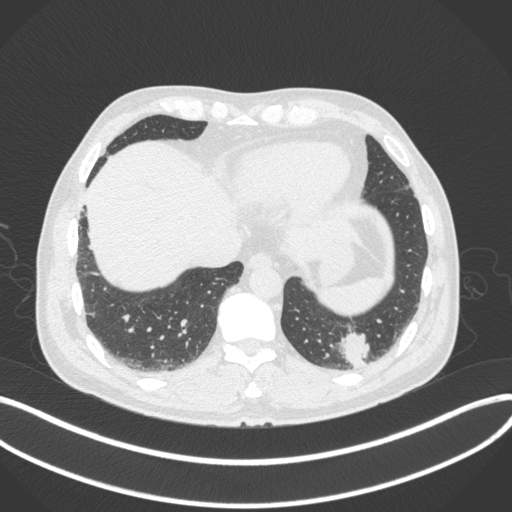
Chest CT, one axial slice; slice 60 of 313 in the series (ordered by position); reconstruction kernel B31f; 120 kVp; lung window (W 1500 / L -600 HU); 512 × 512 image matrix, field of view 400 × 400 mm. Patient: male, 54 years. Case-level facts recorded for this patient, not image findings: clinical TNM (as recorded): T1c N0 M1; histopathological grade: G3.
Structures marked on this image (bounding box drawn by a radiologist):
- lung tumour (recorded histology: adenocarcinoma): bounding box [x1, y1, x2, y2] px = [334, 326, 374, 368]